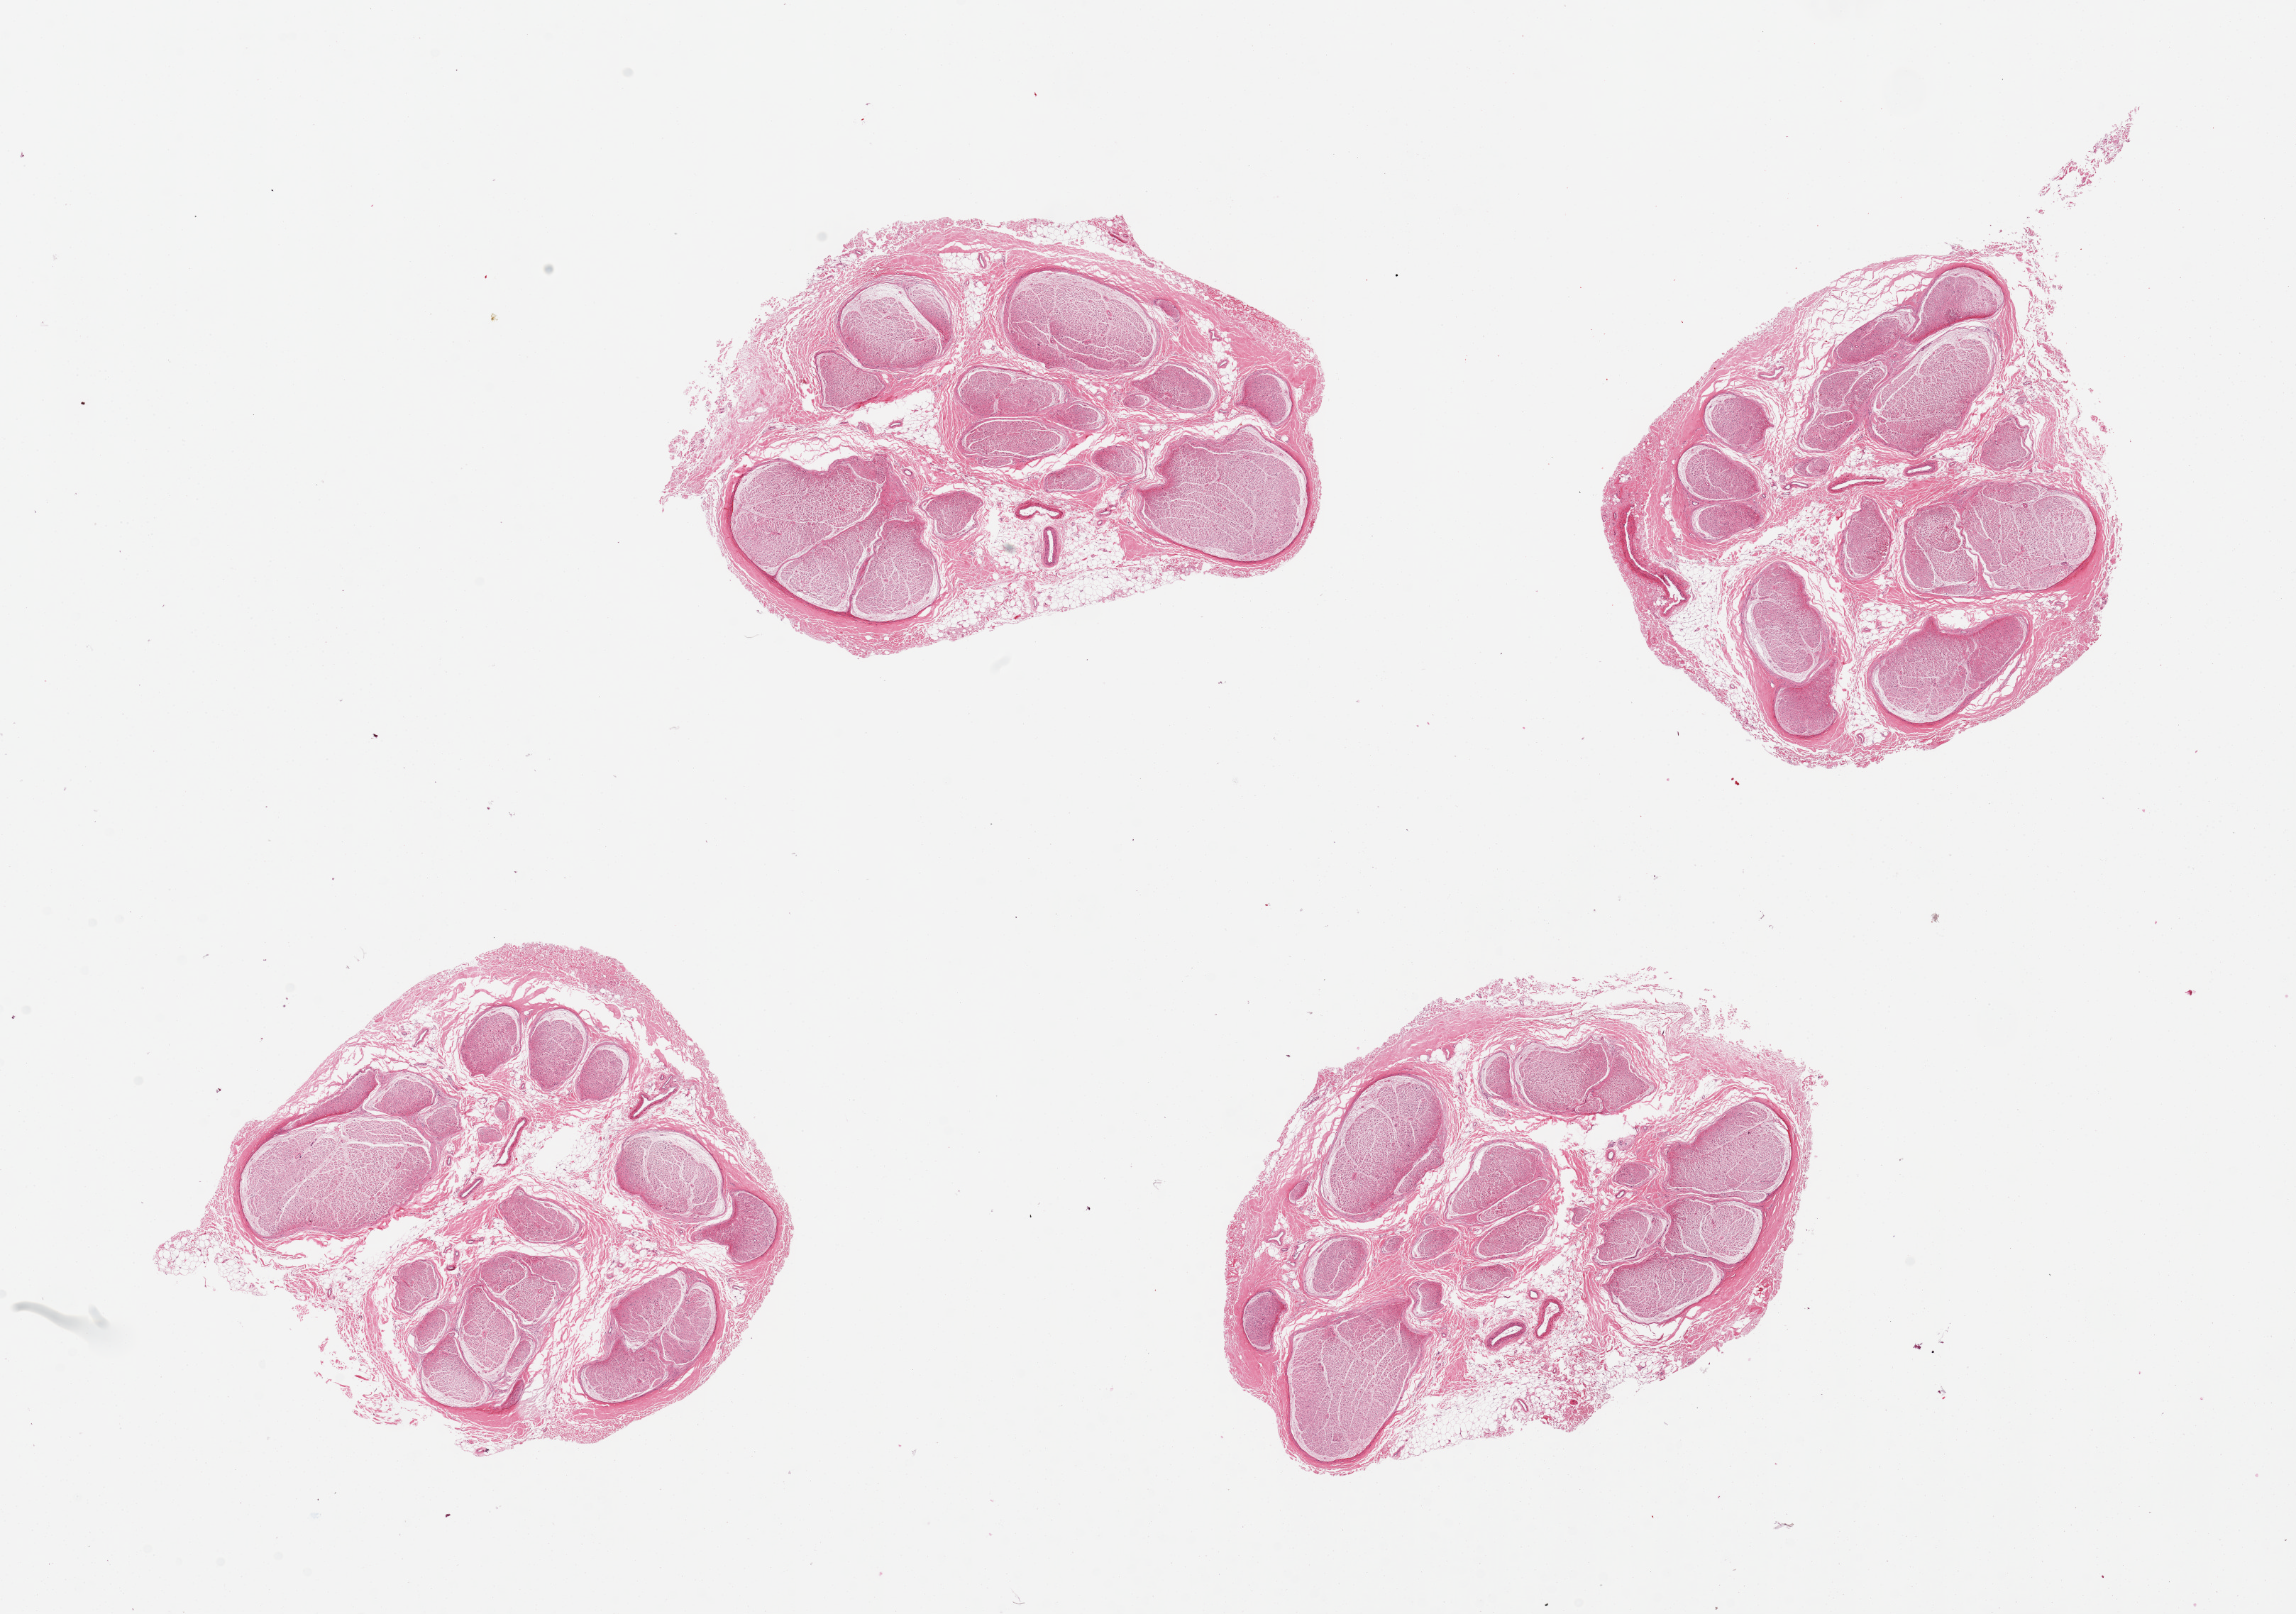
Digitized hematoxylin and eosin (H&E)-stained section — low-resolution overview of the scanned area, about 25.6 x 18.0 mm (from a 20x scan), PAXgene-fixed, paraffin-embedded tissue, section of tibial nerve (target tissue), donor tissue sample. Donor sex: male.
Review note (as recorded): 4 pieces; up to 30% internal and external fat.